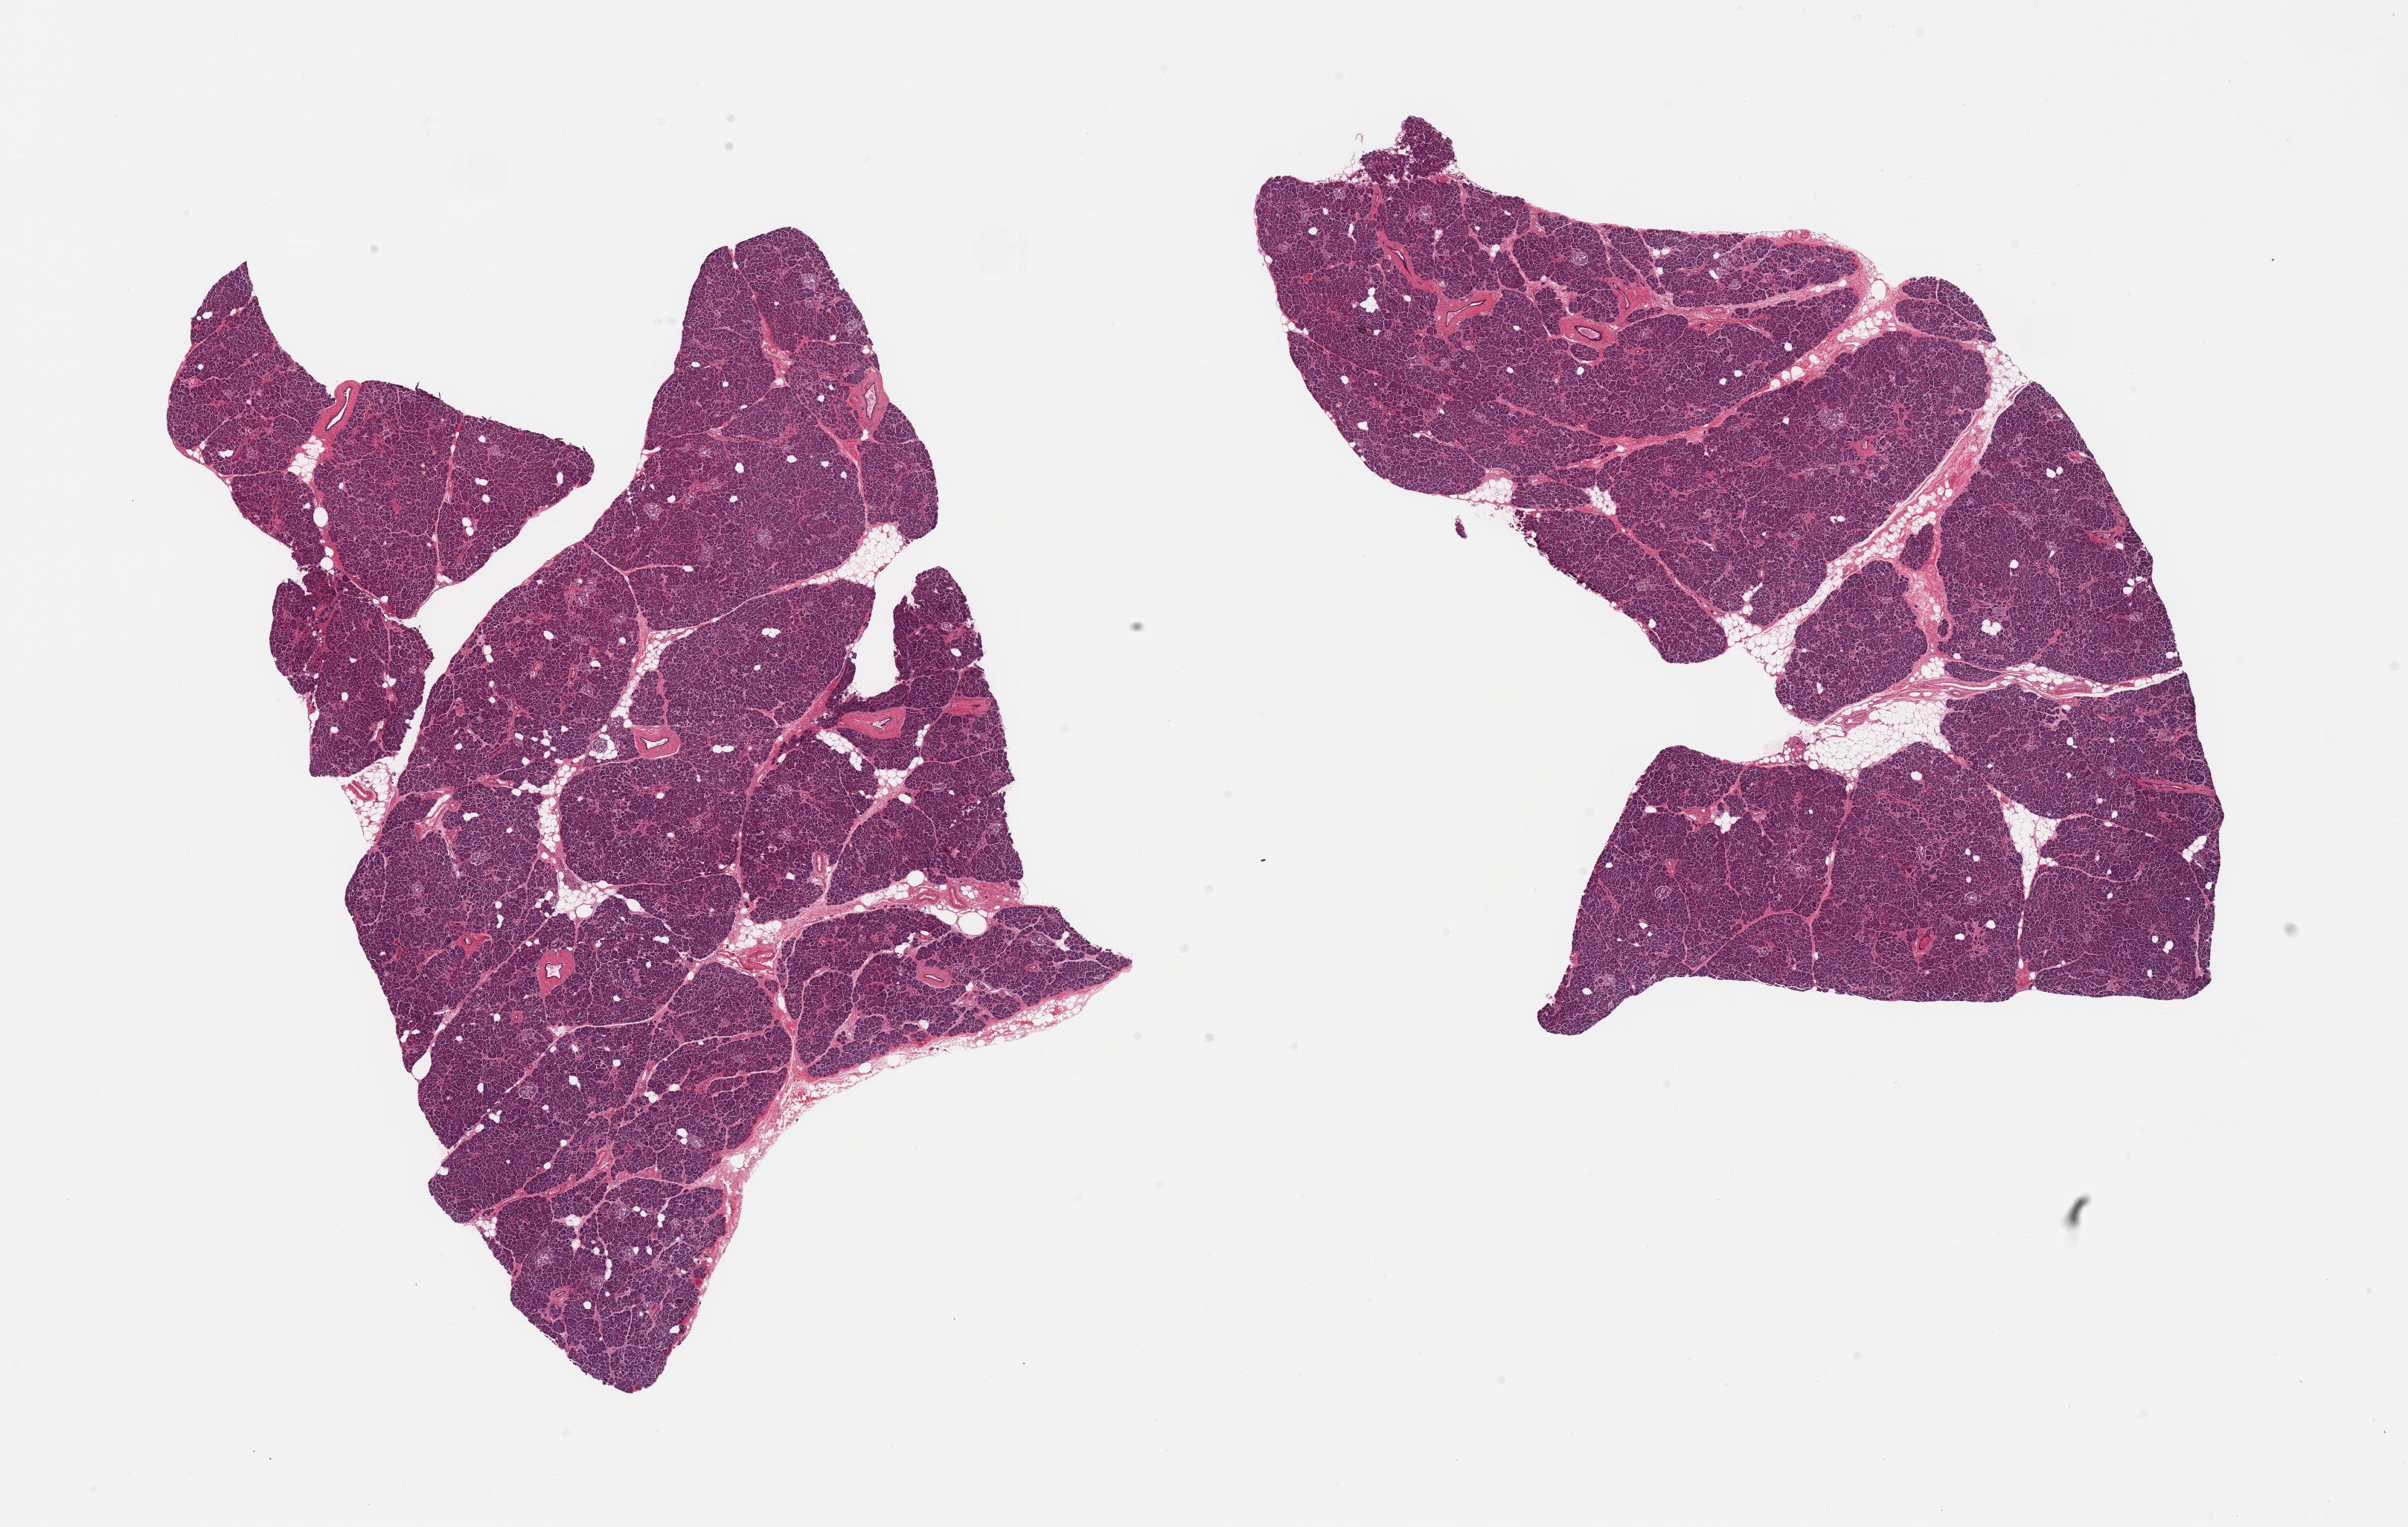
Digitized hematoxylin and eosin (H&E)-stained section, a low-resolution overview of the entire scanned area, about 25.6 x 16.2 mm (from a 20x scan), PAXgene-fixed, paraffin-embedded tissue, sampled site (target tissue): pancreas, tissue donor sample. Donor: female.
Review note (as recorded): 2 pieces; well preserved, islets well visualized, small portion internal fat.